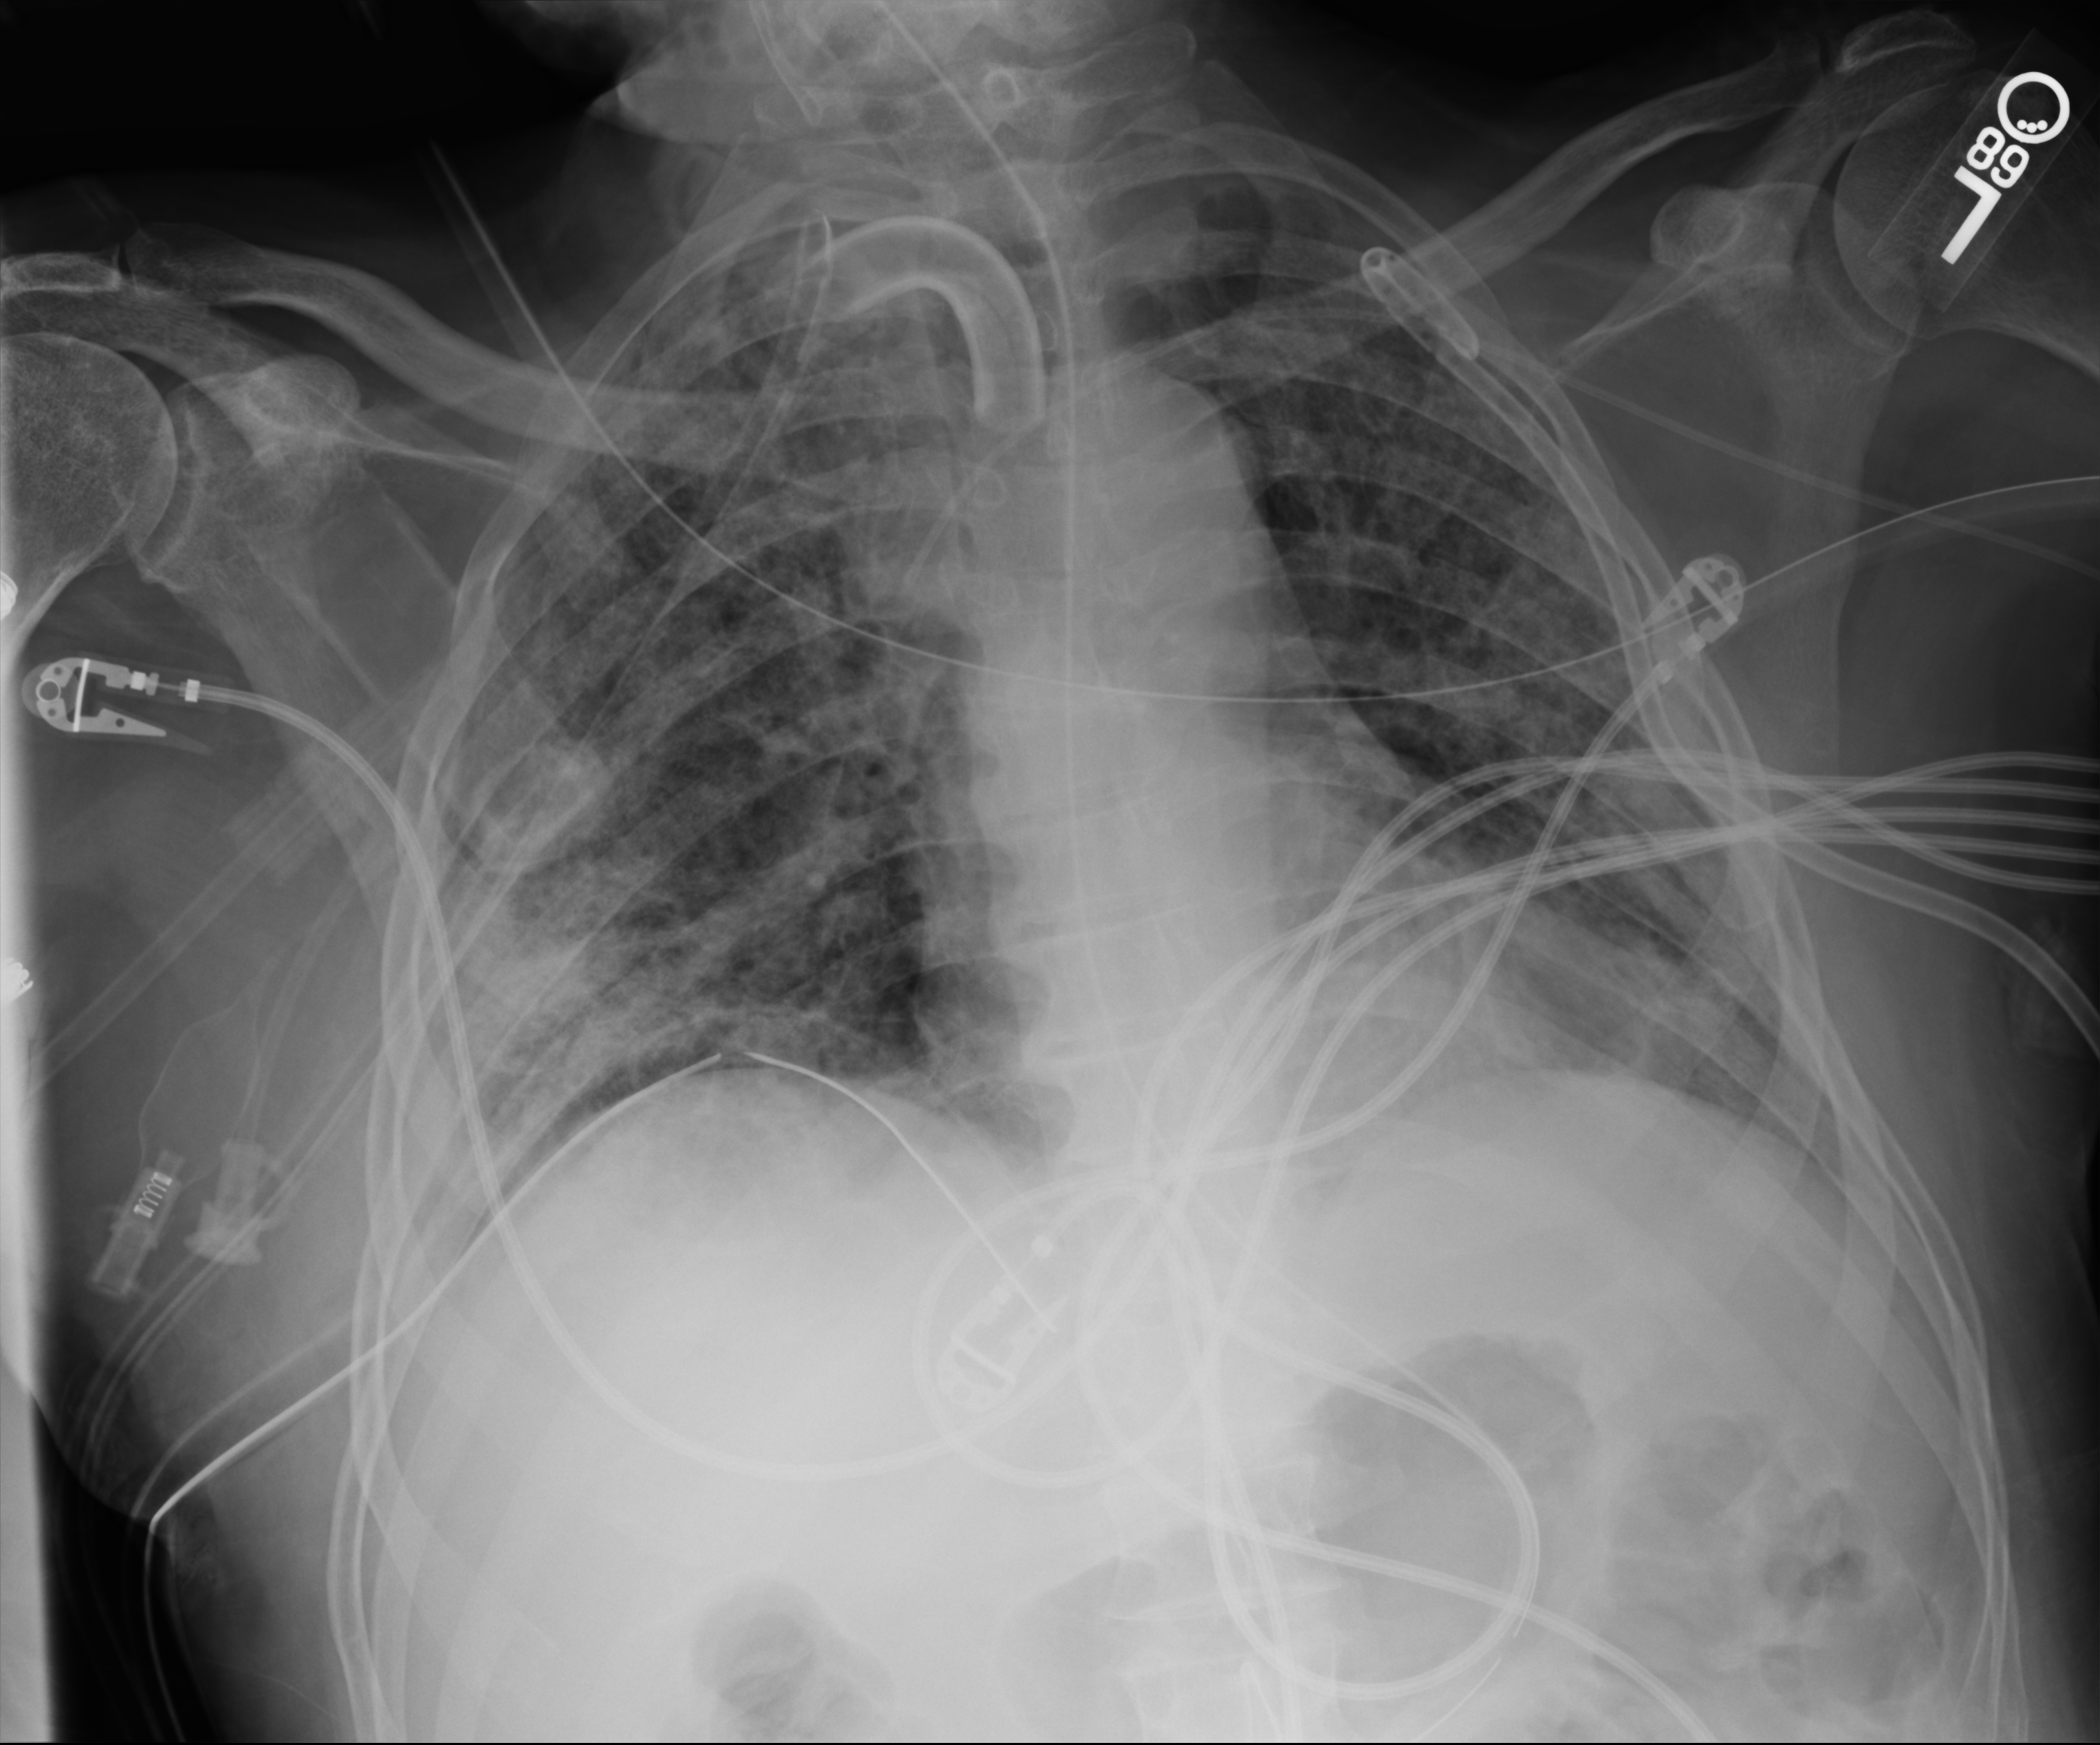
Chest X-ray (portable), anteroposterior (AP) projection. Patient hospitalised with COVID-19; male, aged 18–59 years.
Hospital-stay facts (about this admission, not read from this image; timing relative to this image not recorded):
- admitted to intensive care during this hospital stay: yes